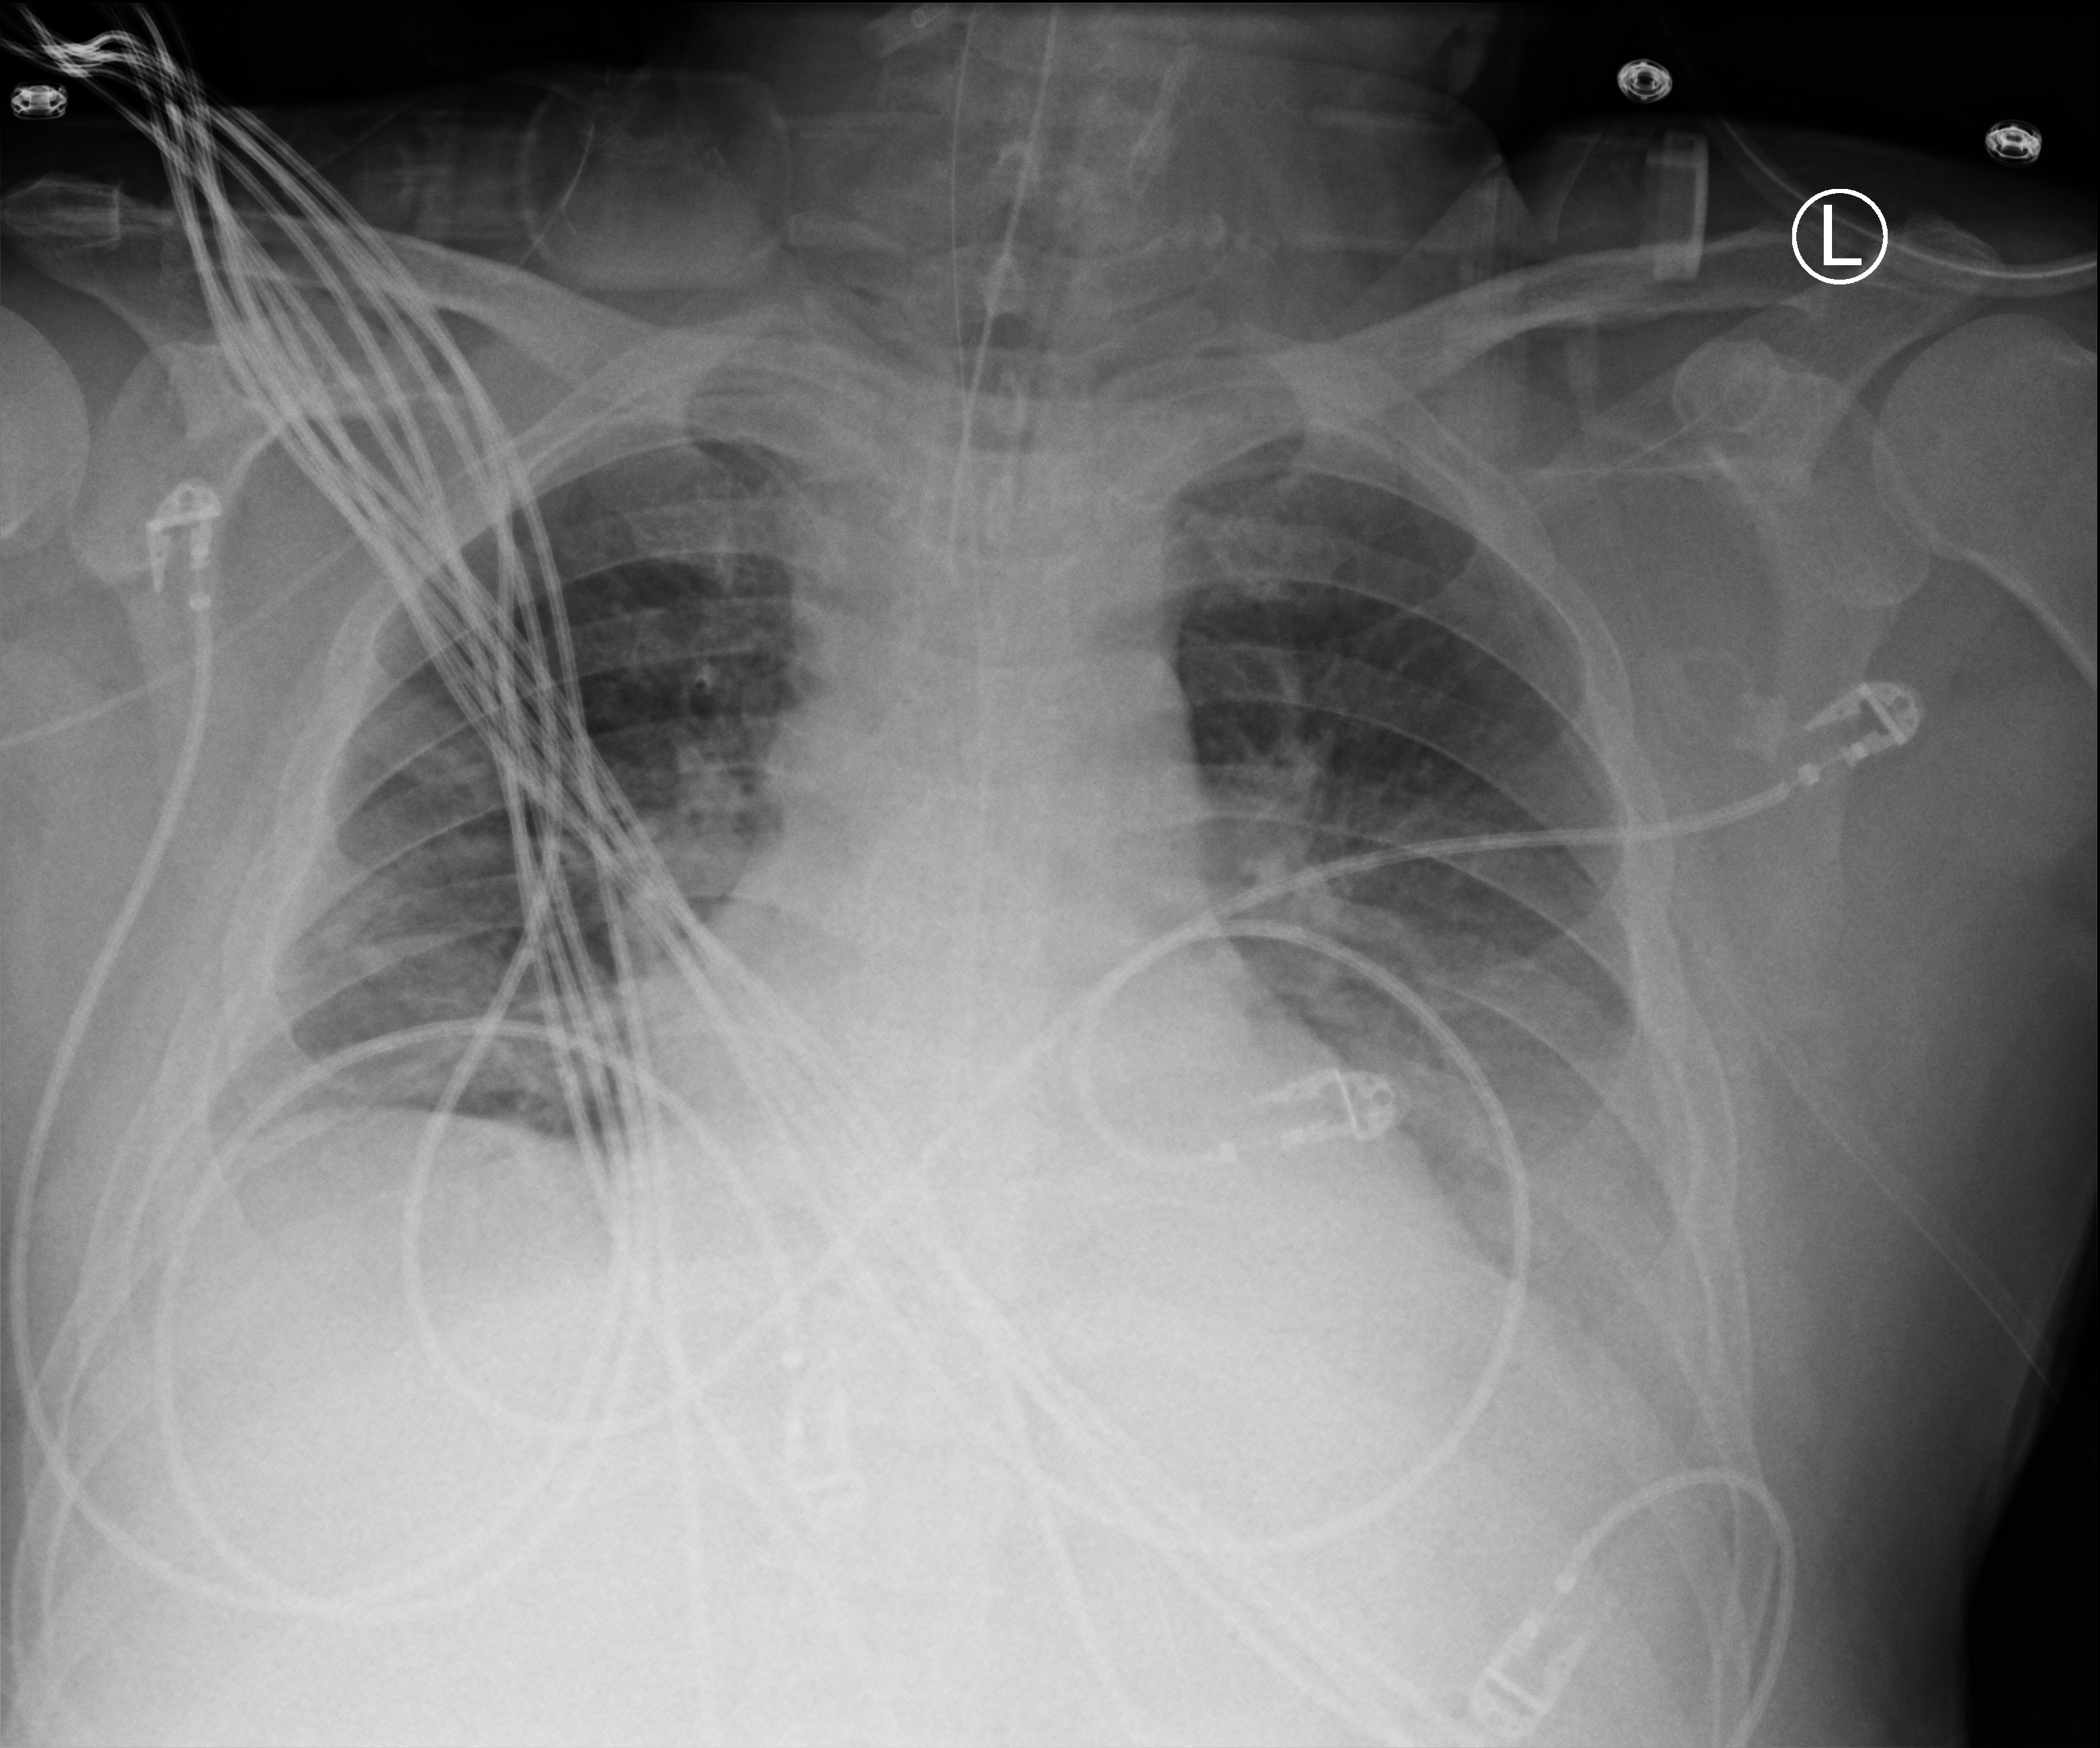
Chest X-ray (portable), anteroposterior (AP) projection. Male patient hospitalised with COVID-19, age 18–59 years.
From the hospital-stay record, not from the radiograph (when in the stay this image was taken is not recorded): mechanically ventilated during this hospital stay: yes; length of hospital stay: 65 days.